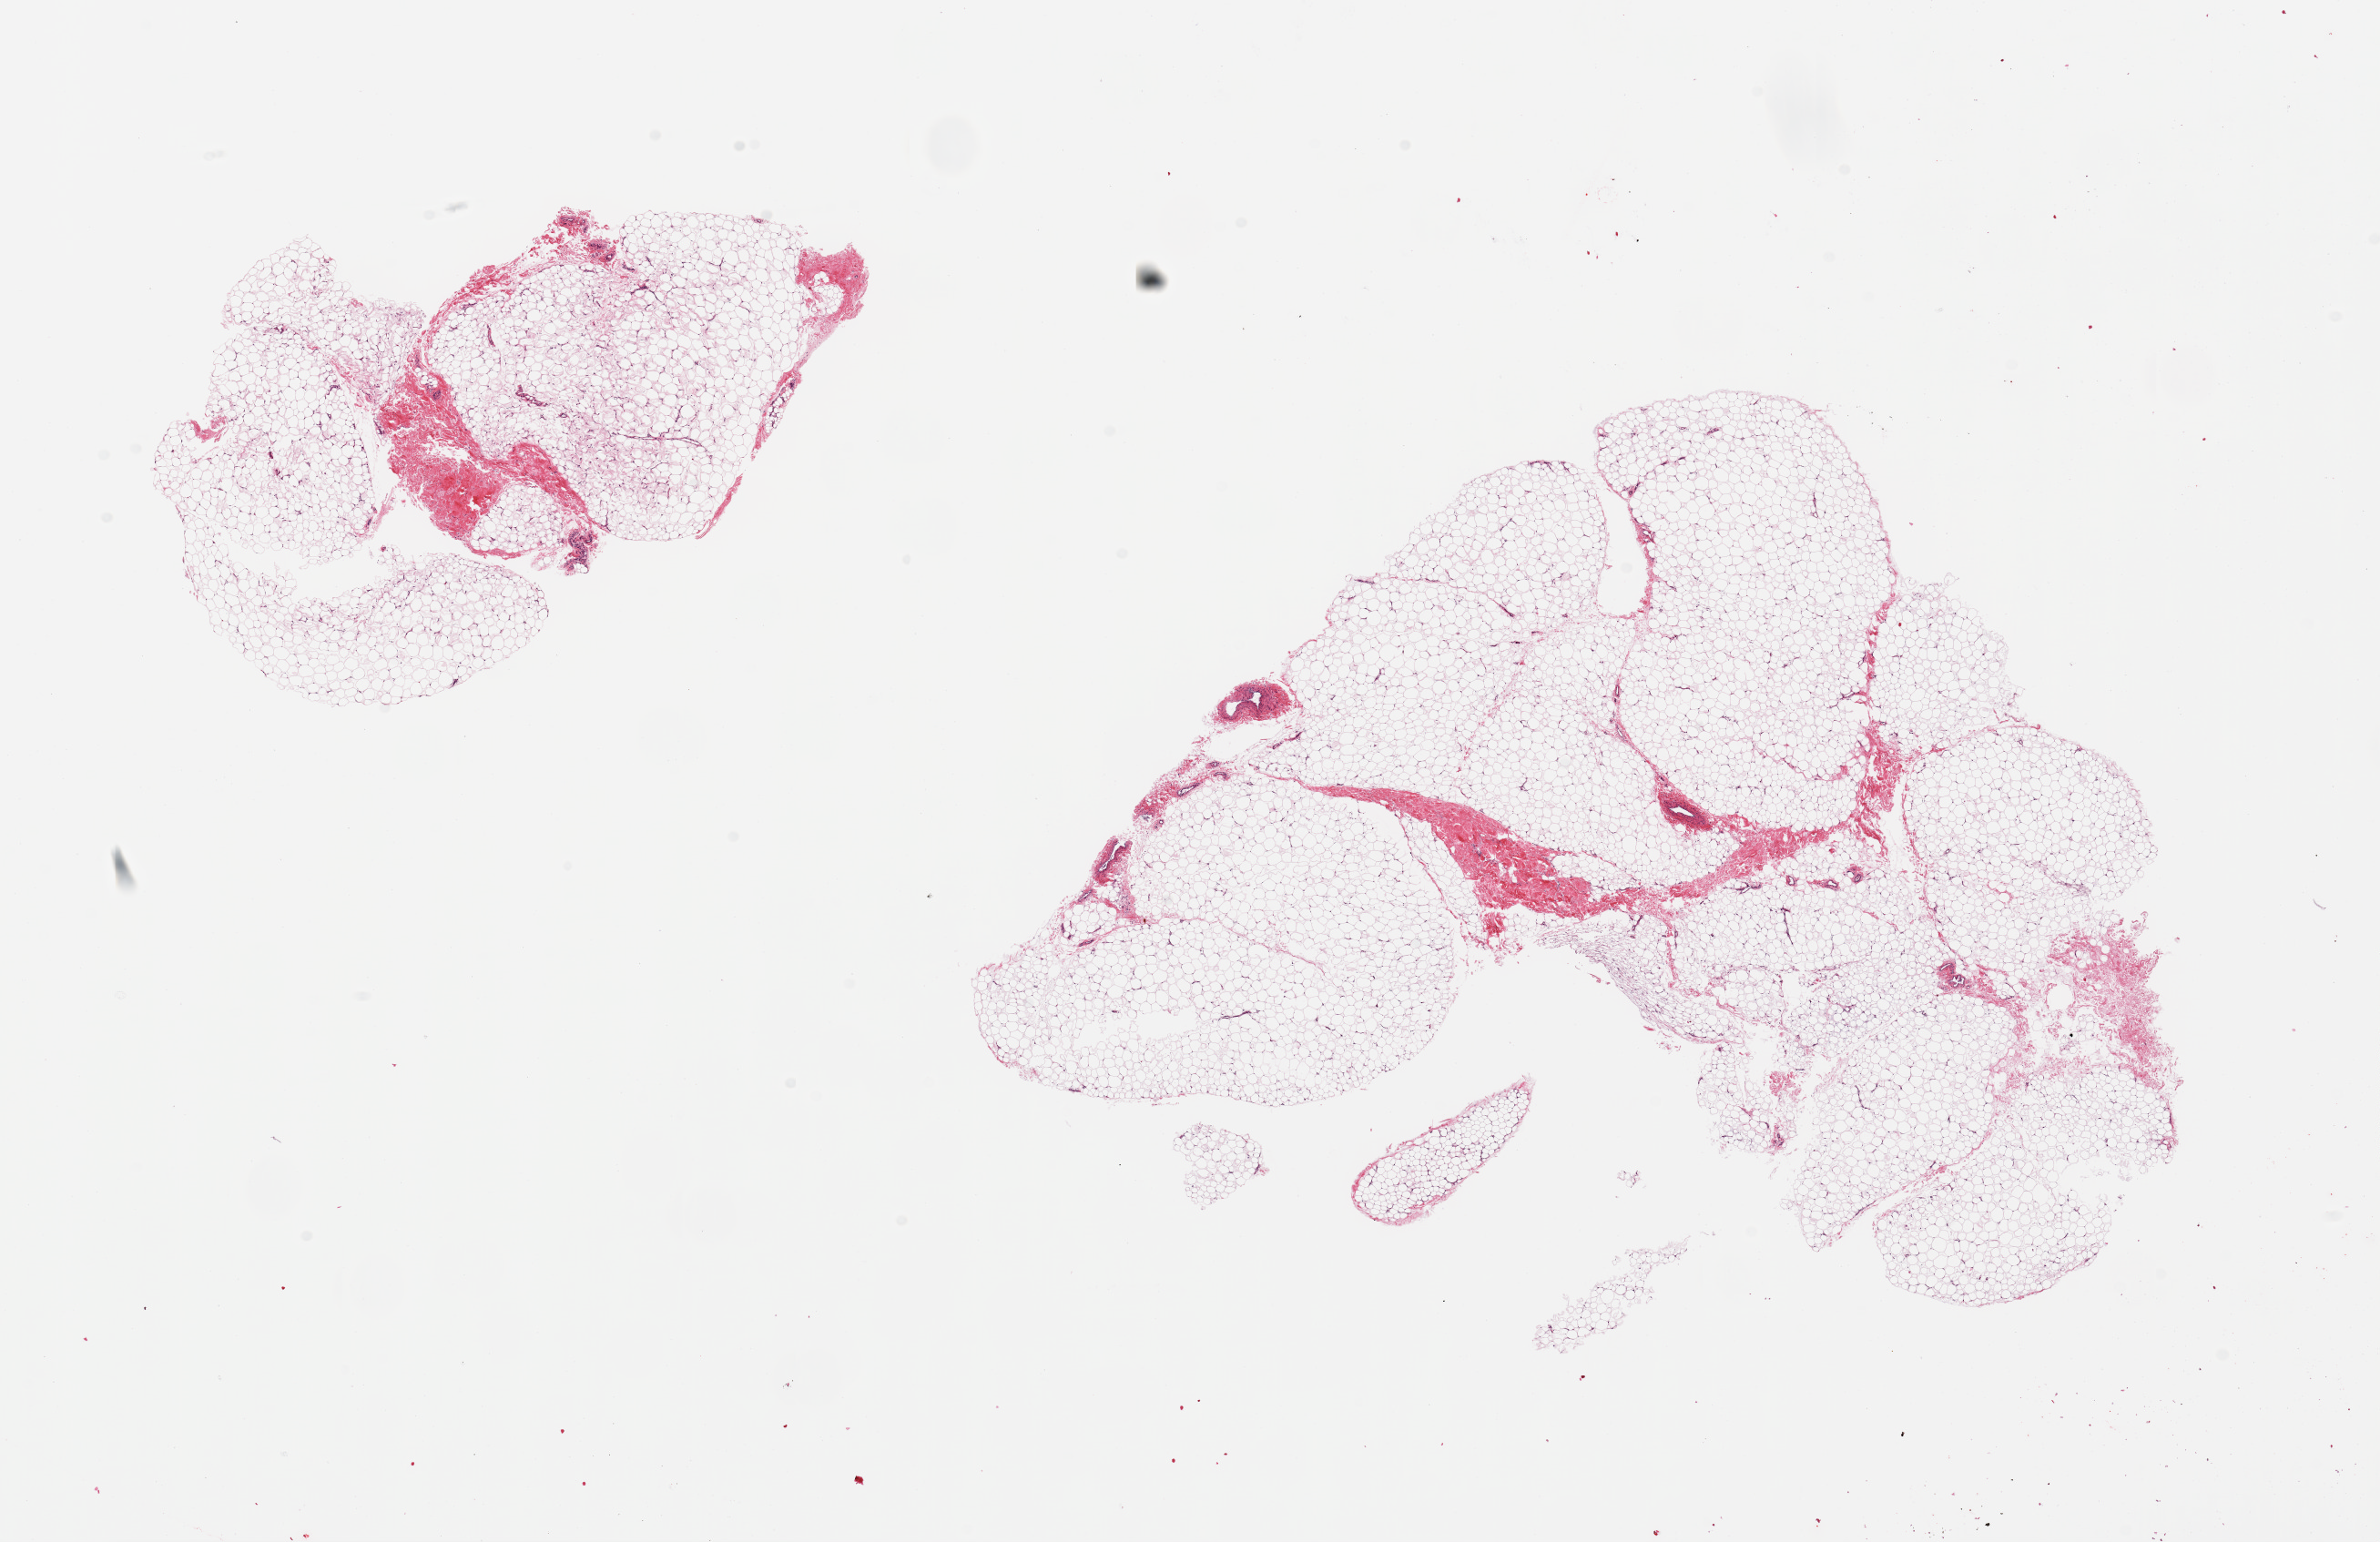
Whole-slide image, H&E stain, brightfield, whole scanned area (about 20.7 x 13.4 mm) shown as a low-resolution overview. PAXgene-fixed, paraffin-embedded tissue. Sampled site (target tissue): adipose tissue. Tissue donor sample.
Review note (as recorded): 2 pieces; fascia/vascular elements are ~10%.